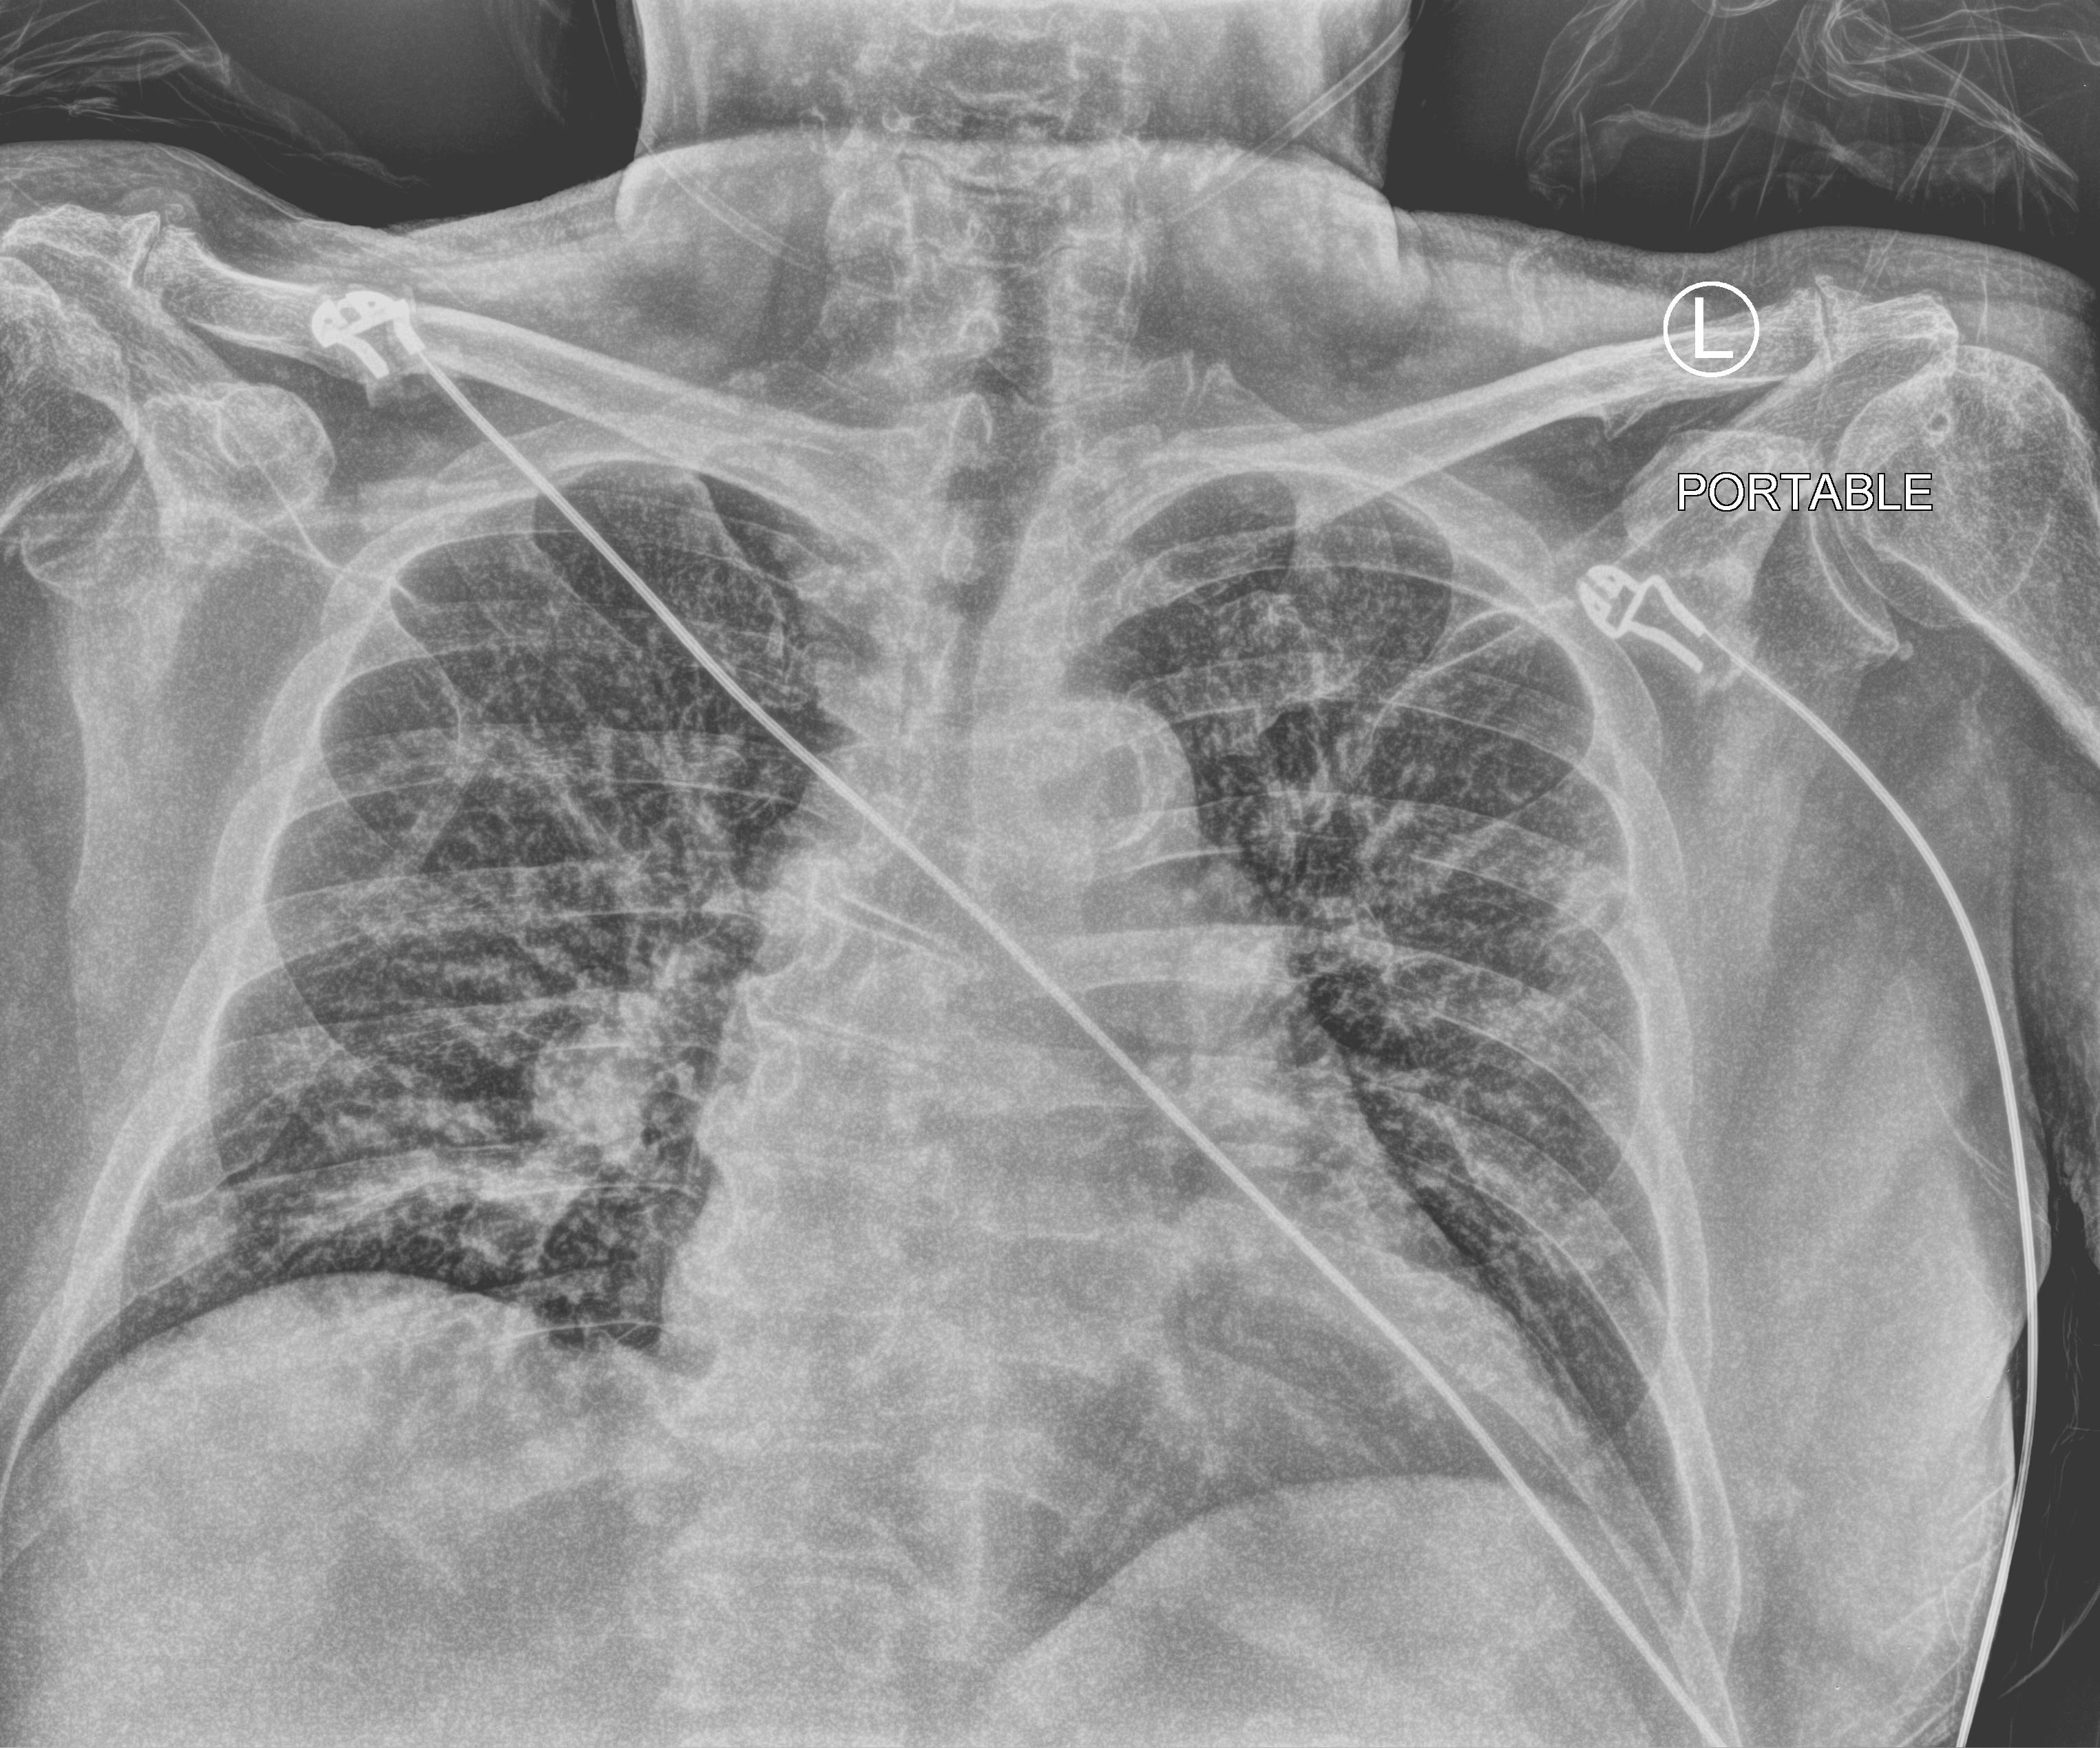
Bedside chest radiograph (computed radiography). Patient hospitalised with COVID-19; male, aged 60–74 years.
From the hospital-stay record, not from the radiograph (when in the stay this image was taken is not recorded):
- mechanically ventilated during this hospital stay: no